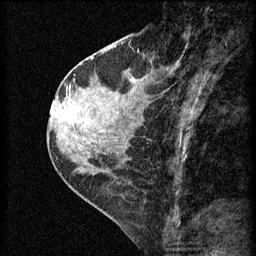
Breast MRI (dynamic contrast-enhanced), one sagittal slice; slice 25 of 60 in the series (ordered by position); 3 images stored at this slice position (order not interpretable as contrast timing); 1.5 T; TE 4.2 ms, TR 8.2 ms; 256 × 256 image matrix. Patient: female, 45 years.
Annotated regions visible in this slice (semi-automatic segmentation, software-assisted and operator-edited):
- analysis volume of interest (the breast-tissue region the enhancement analysis was run in; not a lesion): bounding box <62,98,104,139> (left, top, right, bottom; pixels)
- tumour enhancement mask (voxels above the 70 % enhancement threshold inside the analysis volume of interest): <63,98,71,107>